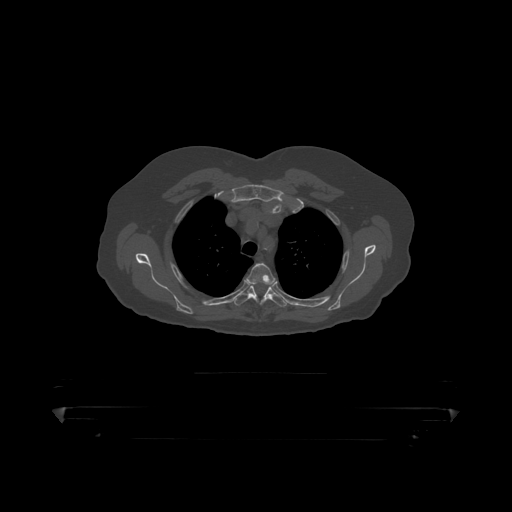
CT including the spine, one axial slice. Slice 348 of 390 in the series (ordered by position). Bone window (W 1800 / L 400 HU). 512 × 512 image matrix, field of view 650 × 650 mm. Male patient, age 60 years. Case-level facts recorded for this patient, not image findings: primary cancer: prostate.
Structures marked on this image (semi-automatic segmentation, software-assisted and operator-edited):
- T3 vertebra: box from (x=246, y=263) to (x=276, y=287) px
- T4 vertebra: (x=234, y=285)–(x=287, y=307)